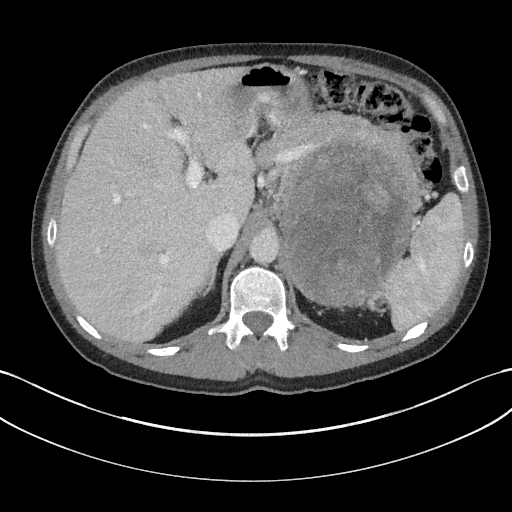
Contrast-enhanced abdominal CT, one axial slice; position 120 of 147 along the scan axis; reconstruction kernel I31f/3; 100 kVp; intravenous contrast given; soft-tissue window (W 400 / L 40 HU); 3 mm slice thickness; 512 × 512 image matrix, field of view 384 × 384 mm. Patient: male, 58 years. From the clinical record (not read from this slice): diagnosis: adrenocortical carcinoma; tumour side: left adrenal; tumour size at pathology: 22 cm.
Outlined on this slice (semi-automatically segmented with operator editing):
- mass: box from (x=278, y=146) to (x=410, y=305) px